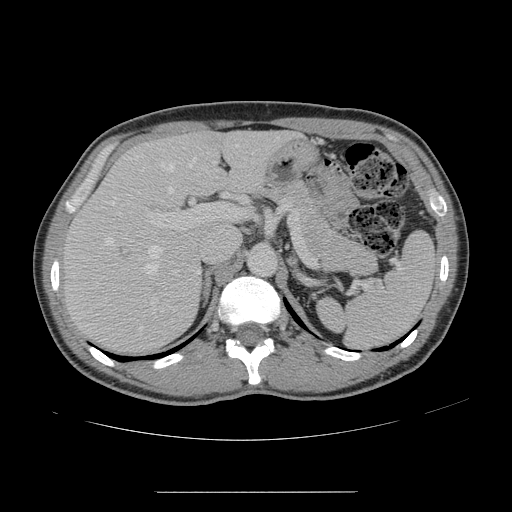
Contrast-enhanced abdominal CT, one axial slice. Position 95 of 178 along the scan axis. 120 kVp. Intravenous contrast given. Soft-tissue window (W 400 / L 40 HU). 2.5 mm slice thickness. 512 × 512 image matrix. Male patient, age 53 years. From the clinical record (not read from this slice): diagnosis: colorectal cancer liver metastases, imaged before liver resection; multiple liver metastases: yes.
Outlined on this slice (expert manual segmentation):
- hepatic veins: bounding box <106,144,238,329> (left, top, right, bottom; pixels)
- liver: <65,131,291,351>
- planned liver remnant (the part of the liver to remain after resection): <147,132,292,193>
- portal vein (with intrahepatic branches): <148,204,246,274>